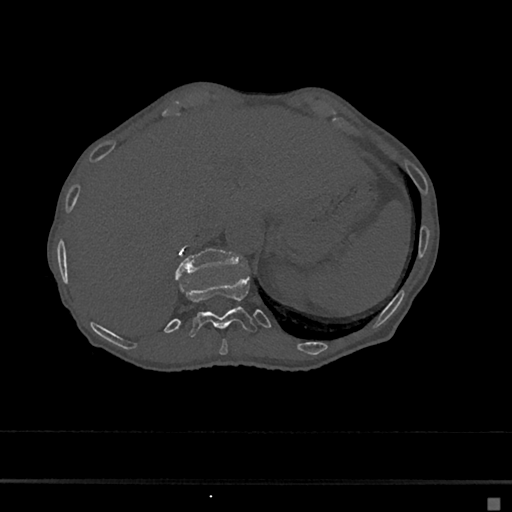
CT including the spine, one axial slice. Slice 171 of 797 in the series (ordered by position). 120 kVp. Bone window (W 1800 / L 400 HU). 0.5 mm slice thickness. 512 × 512 image matrix, field of view 360 × 360 mm. Patient: female, 68 years. Case-level facts recorded for this patient, not image findings: primary cancer: renal.
Outlined on this slice (semi-automatic segmentation, software-assisted and operator-edited):
- T10 vertebra: bounding box [x1, y1, x2, y2] px = [219, 339, 228, 355]
- T11 vertebra: [180, 275, 257, 338]
- T12 vertebra: [175, 247, 238, 279]